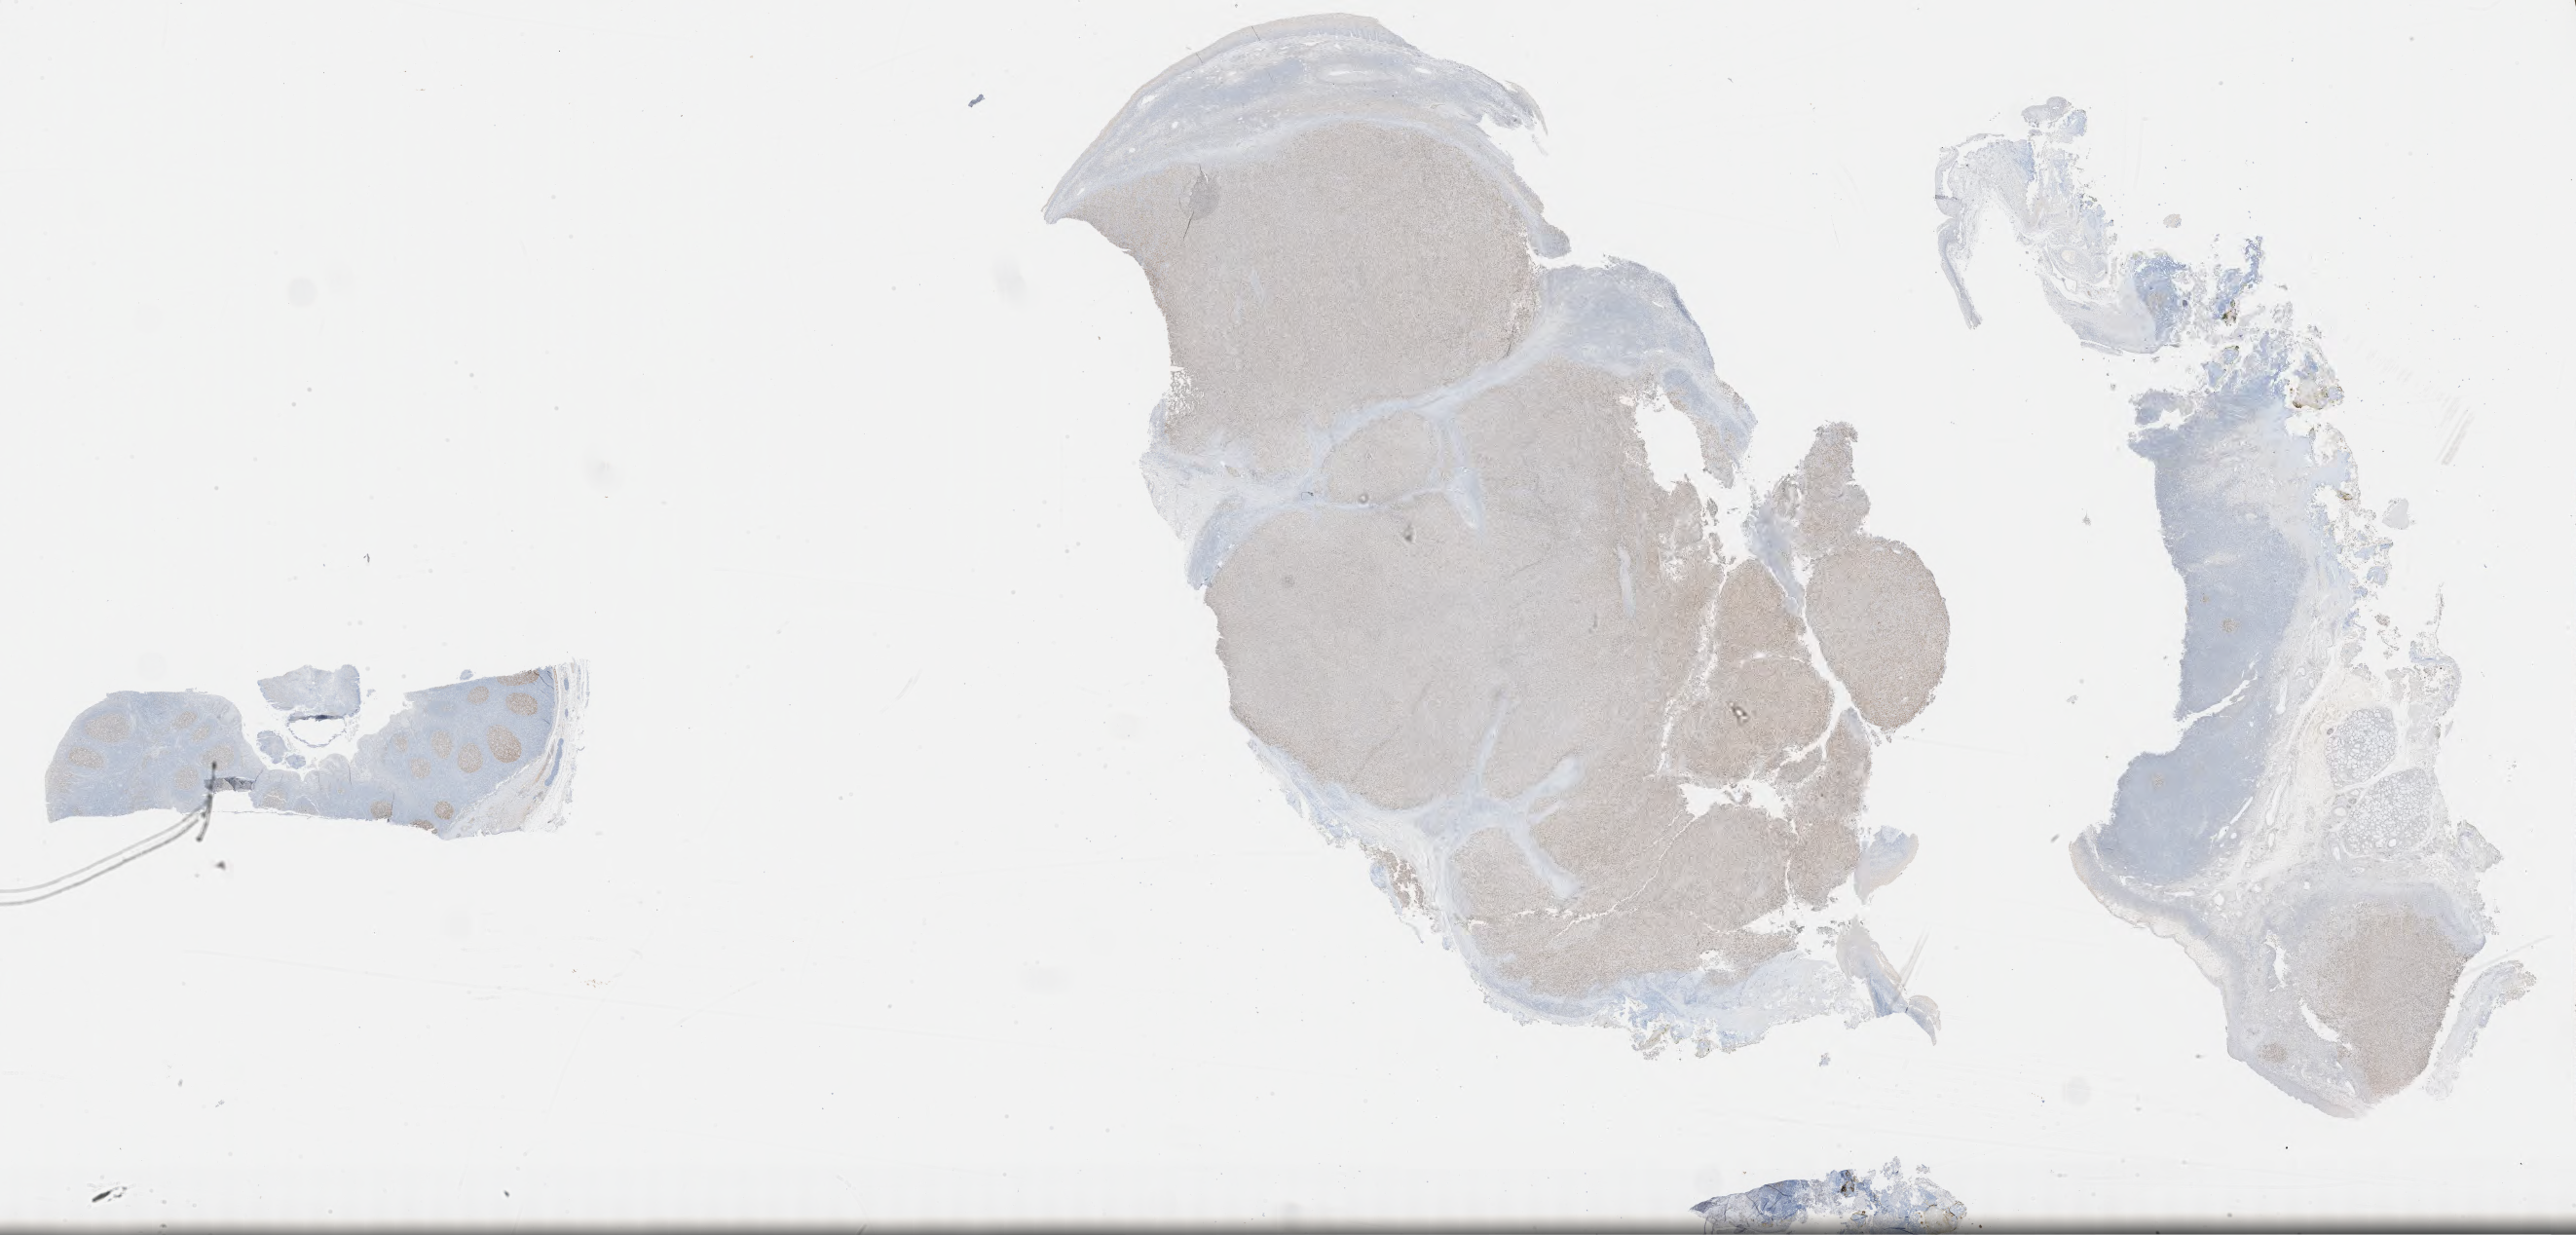
IHC for BCL6, whole-slide image, whole scanned area (about 42.8 x 20.5 mm) shown as a low-resolution overview. Specimen: tumor tissue. Anatomic site: lymph node. Patient male; 56 years old.
• histologic diagnosis: Diffuse large B-cell lymphoma, NOS